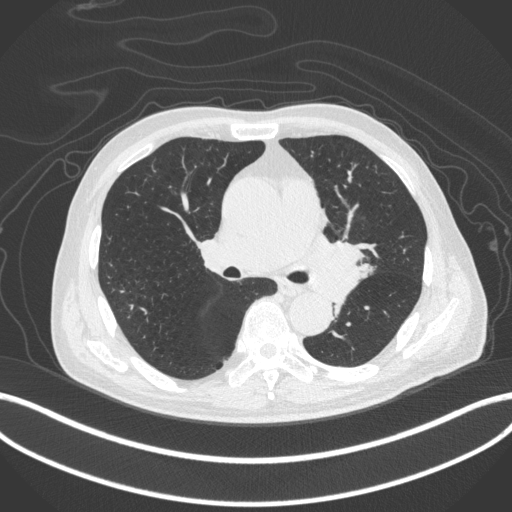
Chest CT, one axial slice; position 252 of 420 along the scan axis; reconstruction kernel B31f; lung window (W 1500 / L -600 HU); 1 mm slice thickness; 512 × 512 image matrix. Male patient, age 77 years. From the clinical record (not read from this slice): clinical TNM (as recorded): T3 N1 M0.
Outlined on this slice (rectangle marked by the reading radiologist):
- lung tumour (recorded histology: adenocarcinoma): bounding box [x1, y1, x2, y2] px = [306, 237, 379, 304]